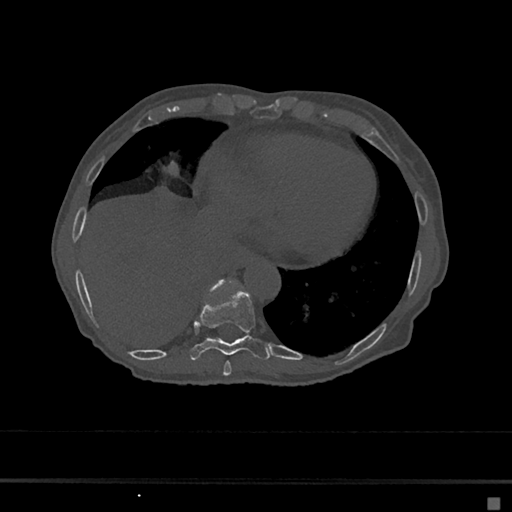
CT including the spine, one axial slice. Position 271 of 797 along the scan axis. Reconstruction kernel Br40s/3. 120 kVp. Bone window (W 1800 / L 400 HU). 512 × 512 image matrix, field of view 360 × 360 mm. Patient: female, 68 years. Case-level facts recorded for this patient, not image findings: primary cancer: renal.
Outlined on this slice (semi-automatic segmentation, software-assisted and operator-edited):
- T10 vertebra: bounding box <208,281,224,294> (left, top, right, bottom; pixels)
- T8 vertebra: <223,361,232,377>
- T9 vertebra: <188,288,272,361>